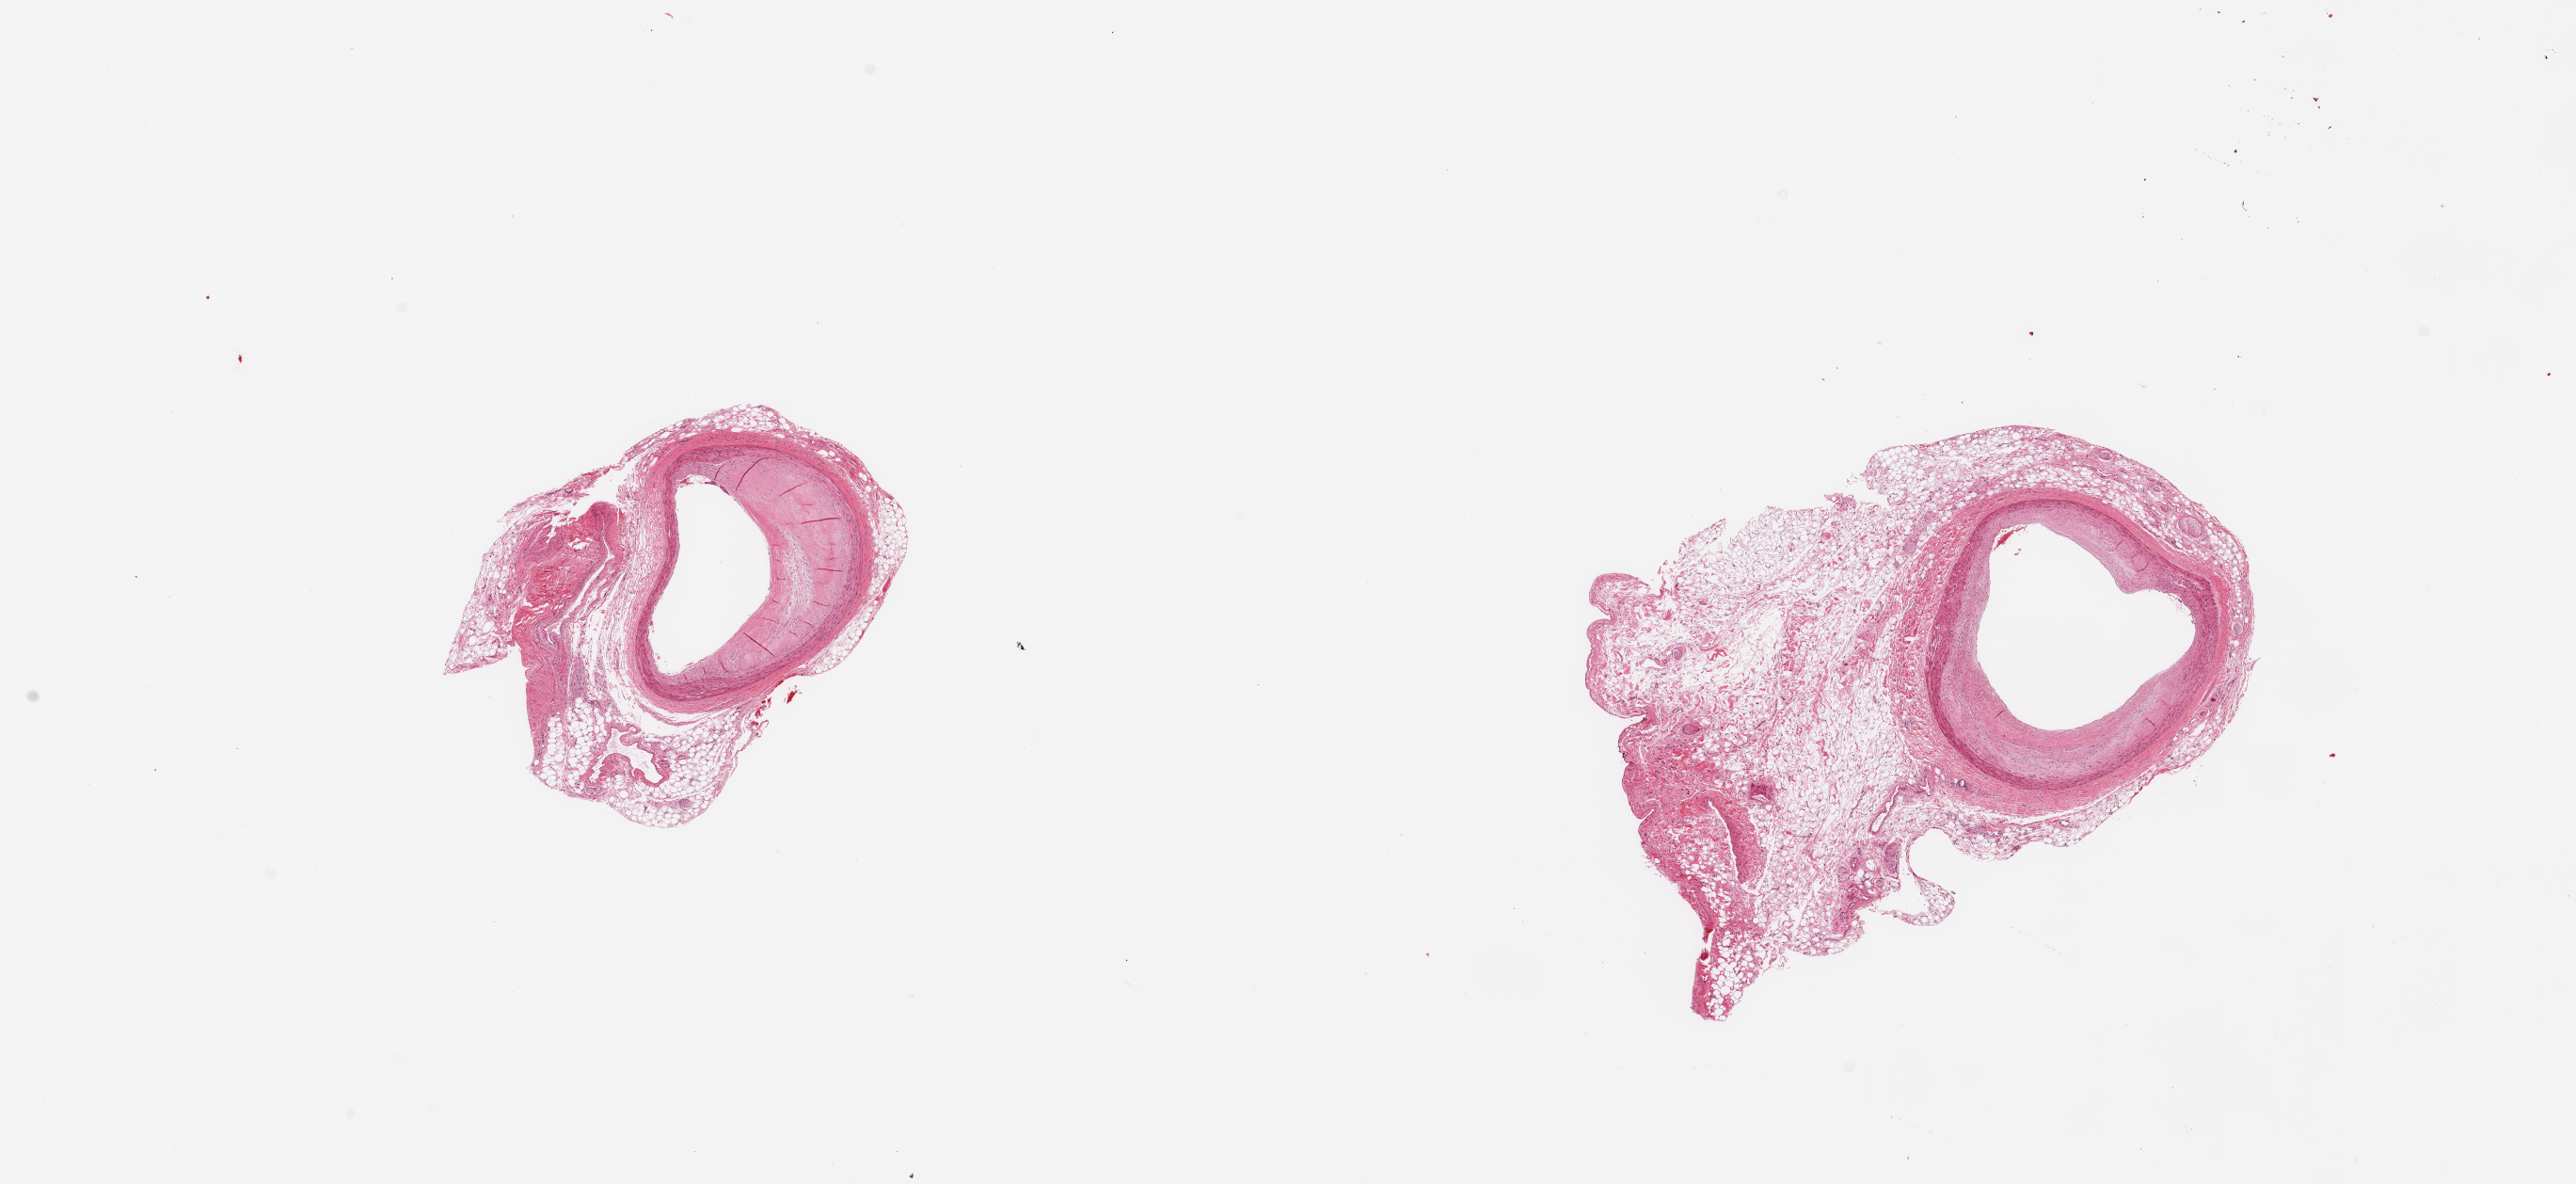
H&E whole-slide image, brightfield, shown as a low-resolution overview of the whole scanned area (about 21.7 x 10.0 mm); PAXgene-fixed, paraffin-embedded tissue; section of coronary artery (target tissue); donor tissue sample.
- reviewer comment on this tissue sample: 2 pieces; atherosclerotic plaque compromising lumen to ~50%; attached fat/vessels/nerve 1.5mm to 2.5mm thick